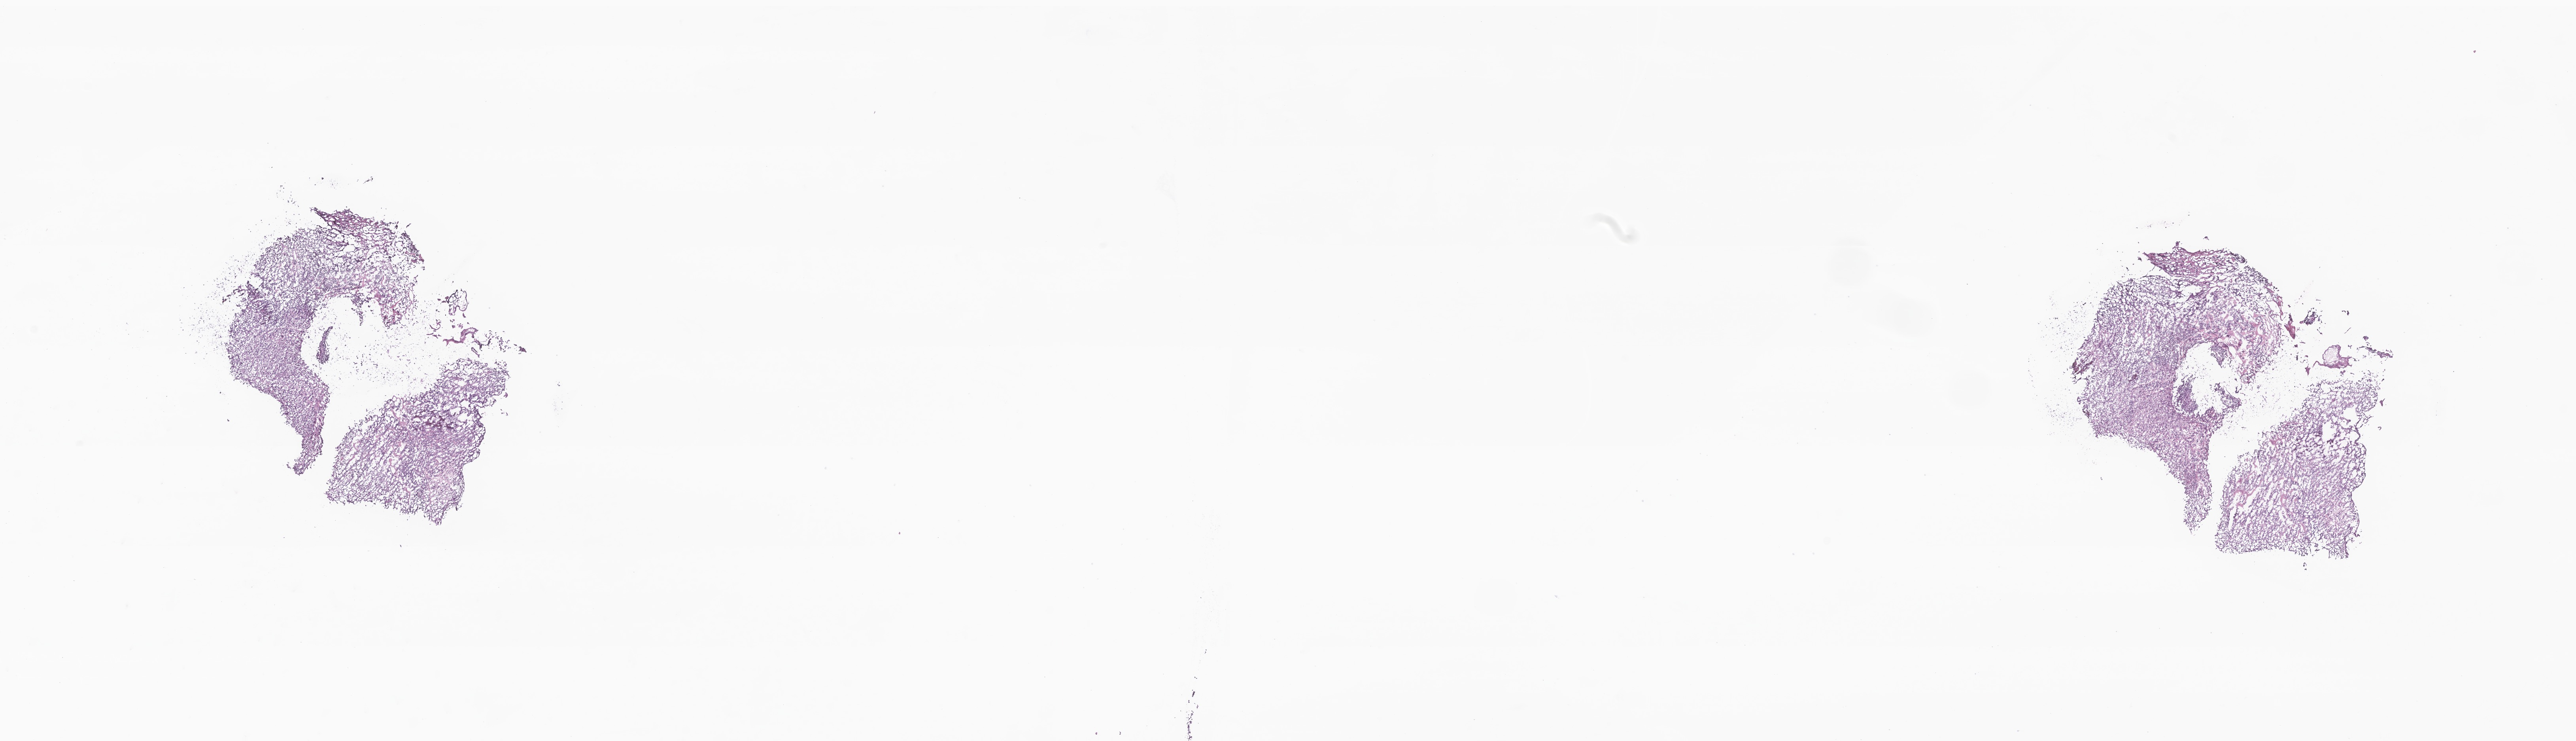
Digitized haematoxylin and eosin-stained section of tumor tissue from the spinal cord — a low-resolution overview of the entire scanned area, about 27.5 x 7.9 mm. Cryosection (OCT / tissue freezing medium). Patient: female, age 172 months (14 years 4 months).
Diagnosis: Neoplasm, malignant.